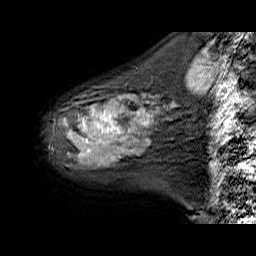
Breast MRI (dynamic contrast-enhanced), one sagittal slice; dynamic contrast-enhanced series, time point 2 of 6 at this slice position (early post-contrast); 1.5 T; TE 6.3 ms, TR 32.9 ms; 4 mm slice thickness; 256 × 256 image matrix, field of view 200 × 200 mm. Female patient. From the clinical record (not read from this slice): setting: breast cancer imaged before/during neoadjuvant chemotherapy; receptor status: HER2-positive.
Structures marked on this image (semi-automatically segmented with operator editing):
- analysis volume of interest (the breast-tissue region the enhancement analysis was run in; not a lesion): box from (x=52, y=94) to (x=176, y=167) px
- tumour enhancement mask (voxels above the 100 % enhancement threshold inside the analysis volume of interest): (x=84, y=112)–(x=147, y=143)